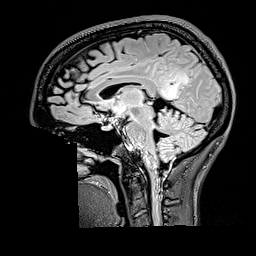
Brain MRI from a brain-tumour surgery series, one sagittal slice. Slice 90 of 176 in the series (ordered by position). T2 FLAIR. 1 mm slice thickness. 256 × 256 image matrix. Case-level facts recorded for this patient, not image findings: histopathology: Oligodendroglioma; WHO grade: 2; IDH mutation: yes; tumour location: Right Parietal.
Annotated regions visible in this slice (expert manual segmentation):
- tumour: bounding box (x1, y1, x2, y2) in pixels: (159, 73, 190, 99)